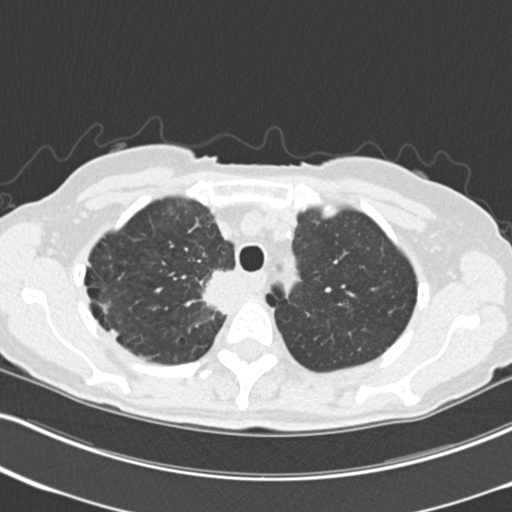
Low-dose screening chest CT, one axial slice. Slice 179 of 226 in the series (ordered by position). Reconstruction kernel B30f. 120 kVp. Lung window (W 1500 / L -600 HU). 2 mm slice thickness. 512 × 512 image matrix, field of view 322 × 322 mm.
Annotated regions visible in this slice (expert manual segmentation):
- lesion 1 (tumor, mediastinum): bounding box [x1, y1, x2, y2] px = [202, 270, 234, 315]